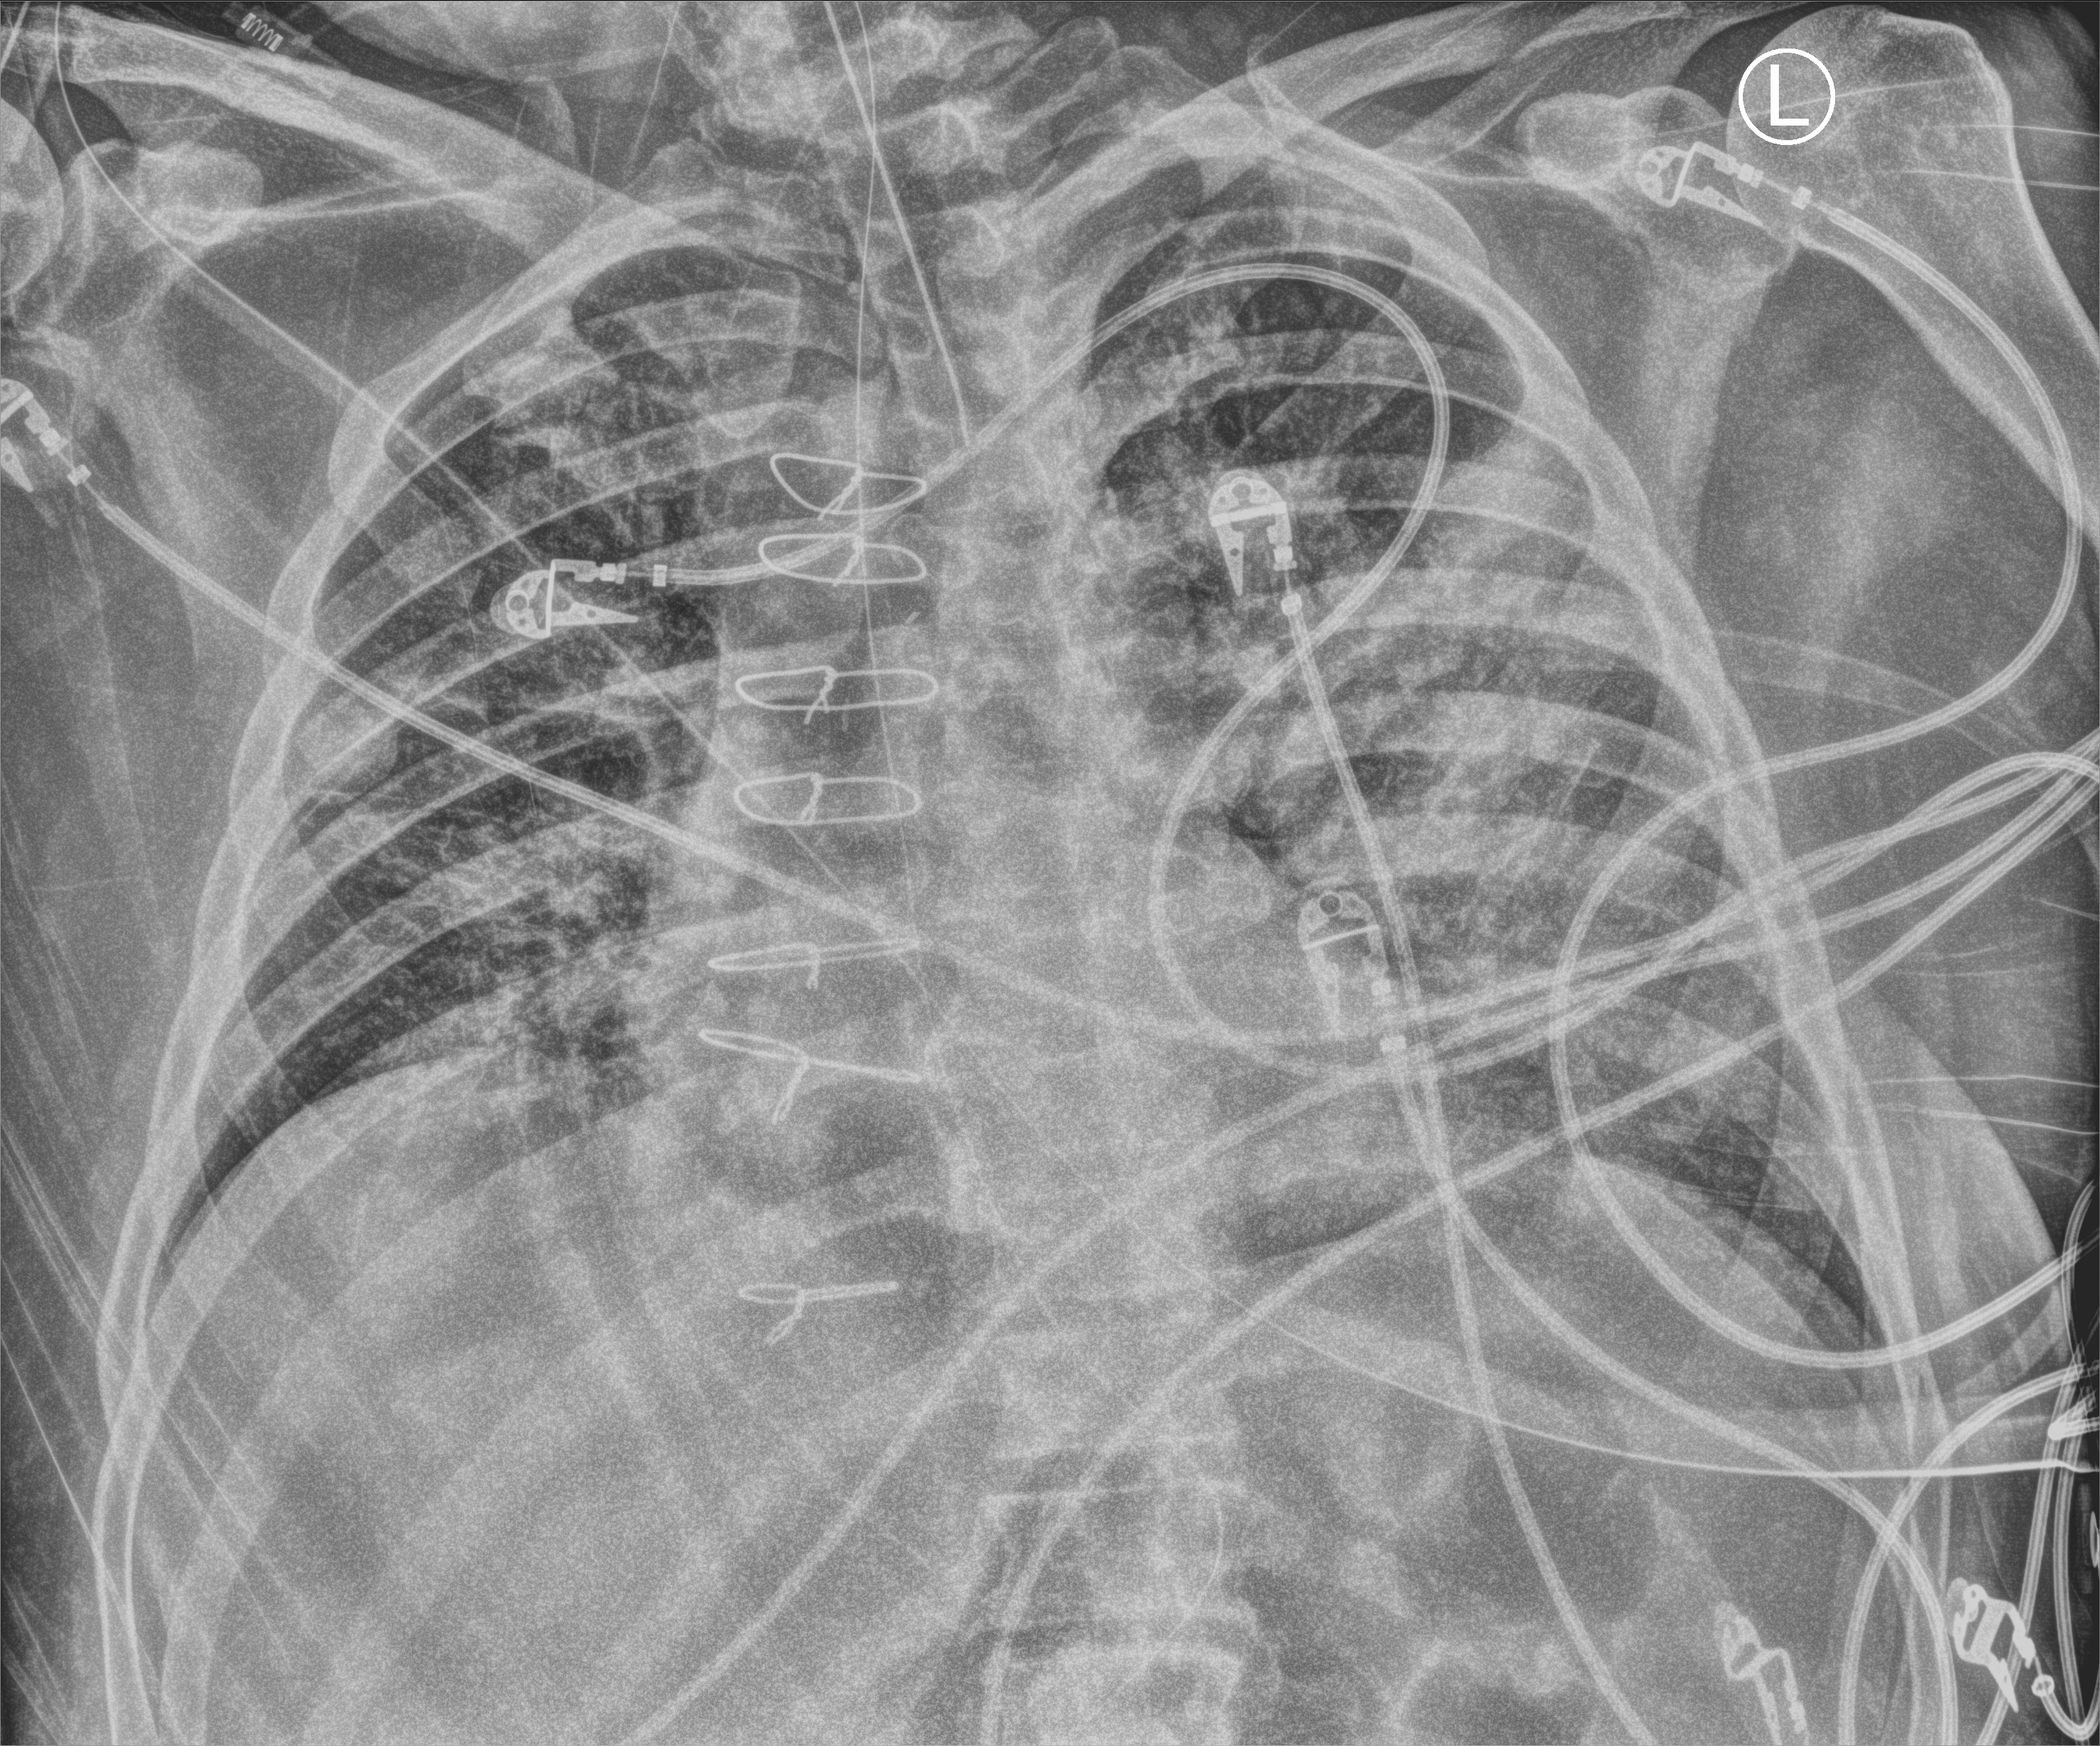
Bedside chest radiograph (computed radiography), anteroposterior (AP) projection. Male patient hospitalised with COVID-19, age 60–74 years.
Admission-level facts for this patient (not findings on this image; timing relative to this image not recorded):
- mechanically ventilated during this hospital stay: yes
- length of hospital stay: 44 days